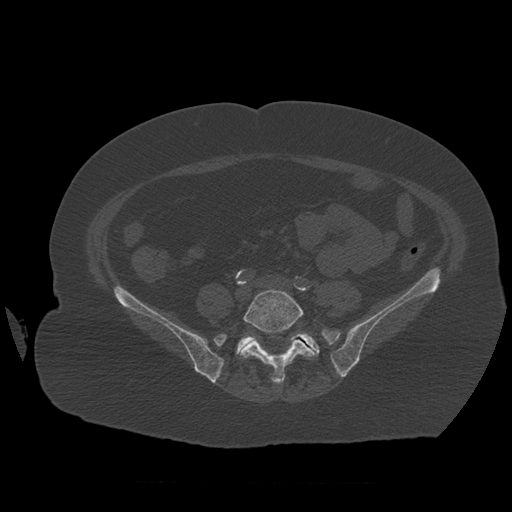
CT including the spine, one axial slice. Position 179 of 399 along the scan axis. 120 kVp. Bone window (W 1800 / L 400 HU). 512 × 512 image matrix, field of view 404 × 404 mm. Patient age 81 years. From the clinical record (not read from this slice): primary cancer: renal.
Annotated regions visible in this slice (semi-automatically segmented with operator editing):
- L5 vertebra: bounding box (x1, y1, x2, y2) in pixels: (241, 289, 317, 384)